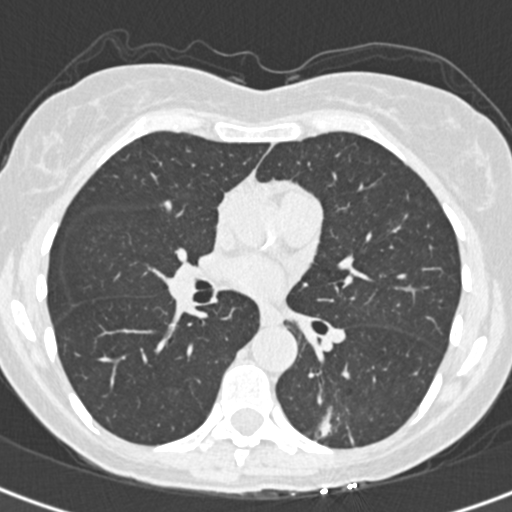
Low-dose screening chest CT, one axial slice; position 186 of 328 along the scan axis; reconstruction kernel B30f; 120 kVp; lung window (W 1500 / L -600 HU); 1 mm slice thickness; 512 × 512 image matrix, field of view 284 × 284 mm.
Structures marked on this image (manually delineated by an expert):
- lesion 1 (tumor, lower lobe of left lung): box from (x=320, y=411) to (x=332, y=437) px